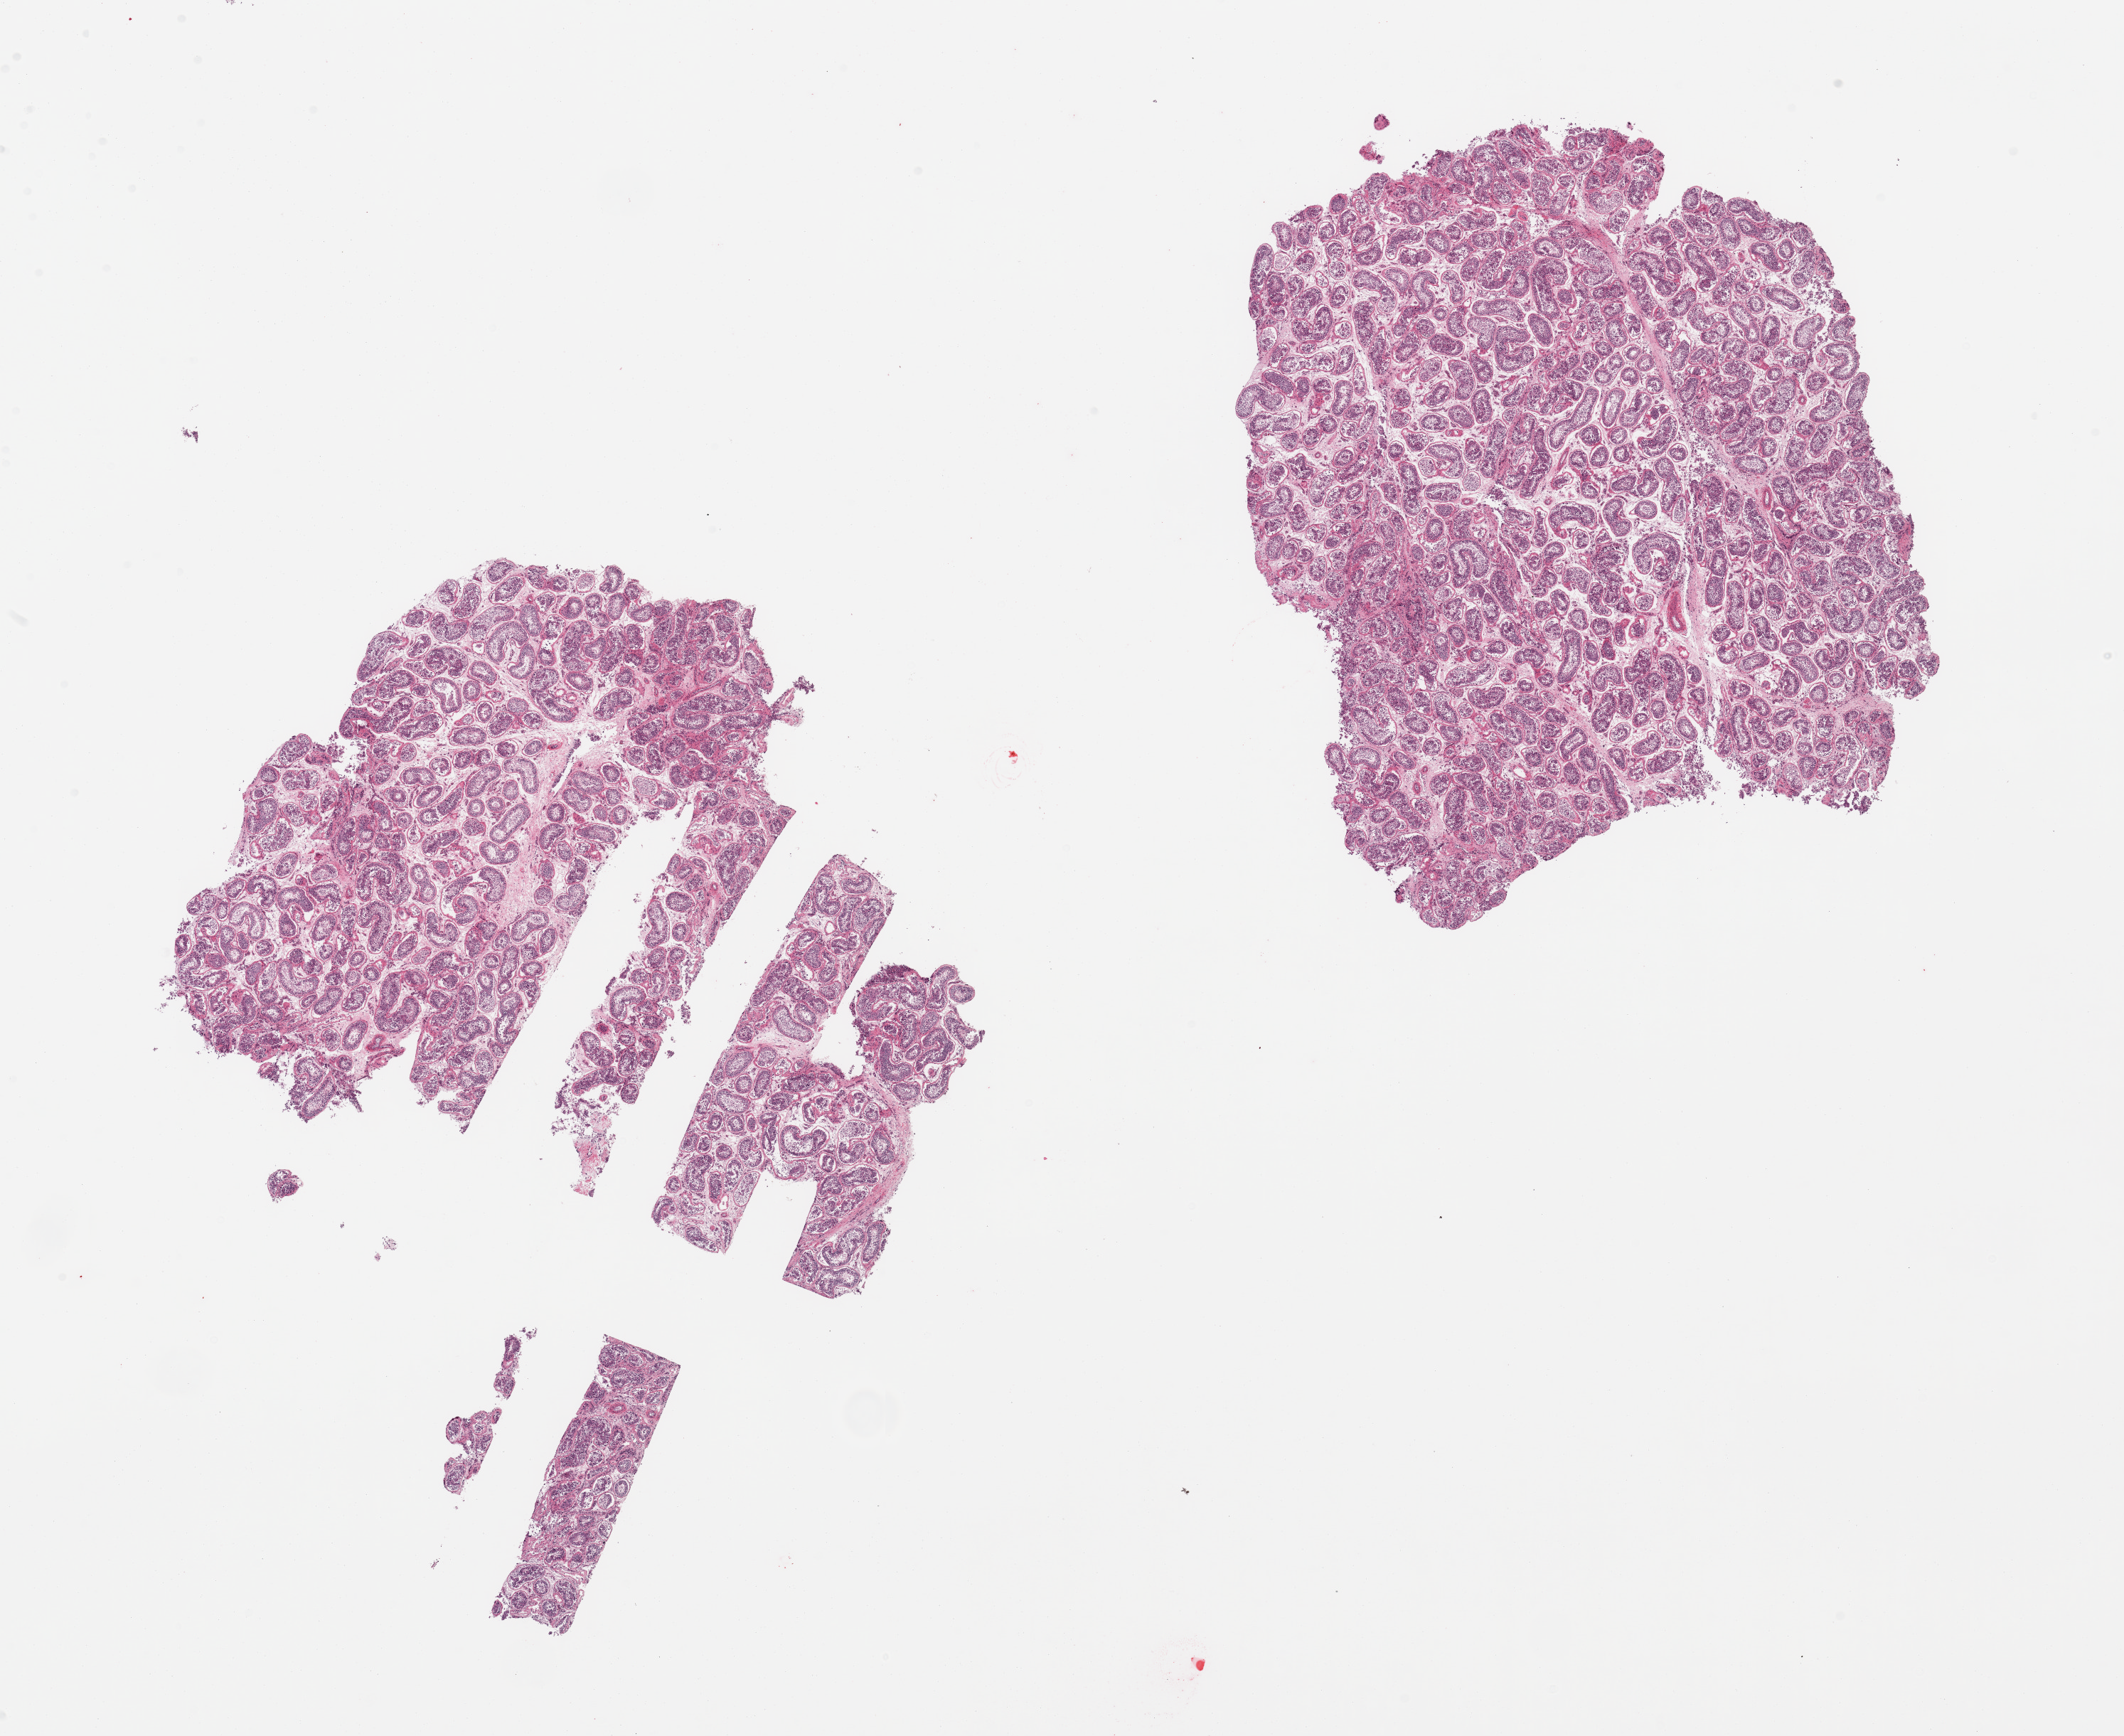
Digitized H&E-stained section — whole scanned area (about 23.6 x 19.3 mm) shown as a low-resolution overview; PAXgene-fixed, paraffin-embedded tissue; target tissue: testis; donor tissue sample.
Pathologist's review note for this sample: 2 pieces; active spermatogenesis.